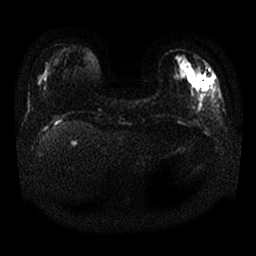
Breast MRI, one axial slice. Position 5 of 25 along the scan axis. Diffusion-weighted series; image 2 of 4 stored at this slice position (different b-values; order by instance number). 1.5 T. 4 mm slice thickness. 256 × 256 image matrix, field of view 340 × 340 mm. Female patient.
Annotated regions visible in this slice (expert manual segmentation):
- tumour on diffusion-weighted imaging: bounding box (x1, y1, x2, y2) in pixels: (194, 73, 214, 91)